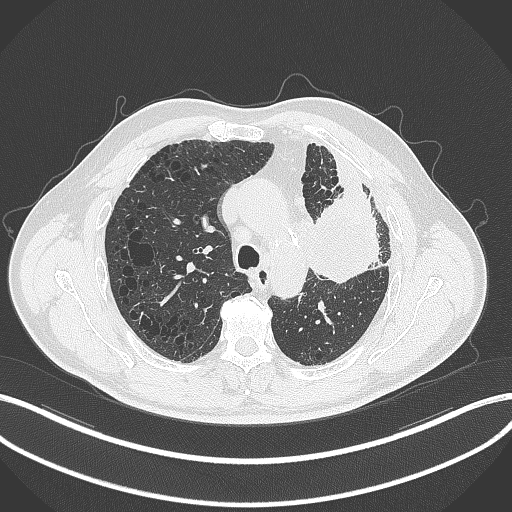
Chest CT, one axial slice; slice 219 of 297 in the series (ordered by position); lung window (W 1500 / L -600 HU); 1 mm slice thickness; 512 × 512 image matrix. Patient: male, 68 years. Case-level facts recorded for this patient, not image findings: clinical TNM (as recorded): T3 N3 M1.
Outlined on this slice (bounding box drawn by a radiologist):
- lung tumour (recorded histology: adenocarcinoma): box from (x=312, y=184) to (x=386, y=283) px